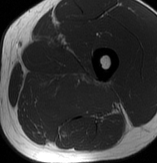
MRI of an extremity soft-tissue mass, one axial slice. MR volume resampled by the dataset authors to the PET/CT grid (not the native acquisition matrix). 3.27 mm slice thickness. 157 × 163 image matrix, field of view 153 × 159 mm. Male patient. Case-level facts recorded for this patient, not image findings: histological type: extraskeletal osteosarcoma; grade: high; site of the primary tumour: left adductur.
Annotated regions visible in this slice (expert contour drawn on MRI and transferred to this co-registered scan by the dataset authors):
- gross tumour volume (mass): bounding box (x1, y1, x2, y2) in pixels: (26, 72, 123, 125)